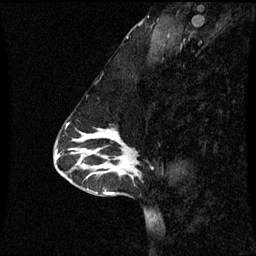
Breast MRI (dynamic contrast-enhanced), one sagittal slice; dynamic contrast-enhanced series, image 2 of 3 at this slice position (ordered by acquisition); 1.5 T; TE 4.2 ms, TR 8.9 ms; 2 mm slice thickness; 256 × 256 image matrix, field of view 220 × 220 mm. Patient: female, 43 years. From the clinical record (not read from this slice): setting: breast cancer imaged before/during neoadjuvant chemotherapy; receptor status: HR-positive, HER2-negative.
Structures marked on this image (semi-automatically segmented with operator editing):
- analysis volume of interest (the breast-tissue region the enhancement analysis was run in; not a lesion): bounding box (x1, y1, x2, y2) in pixels: (84, 130, 139, 171)
- tumour enhancement mask (voxels above the 70 % enhancement threshold inside the analysis volume of interest): (100, 130, 120, 165)